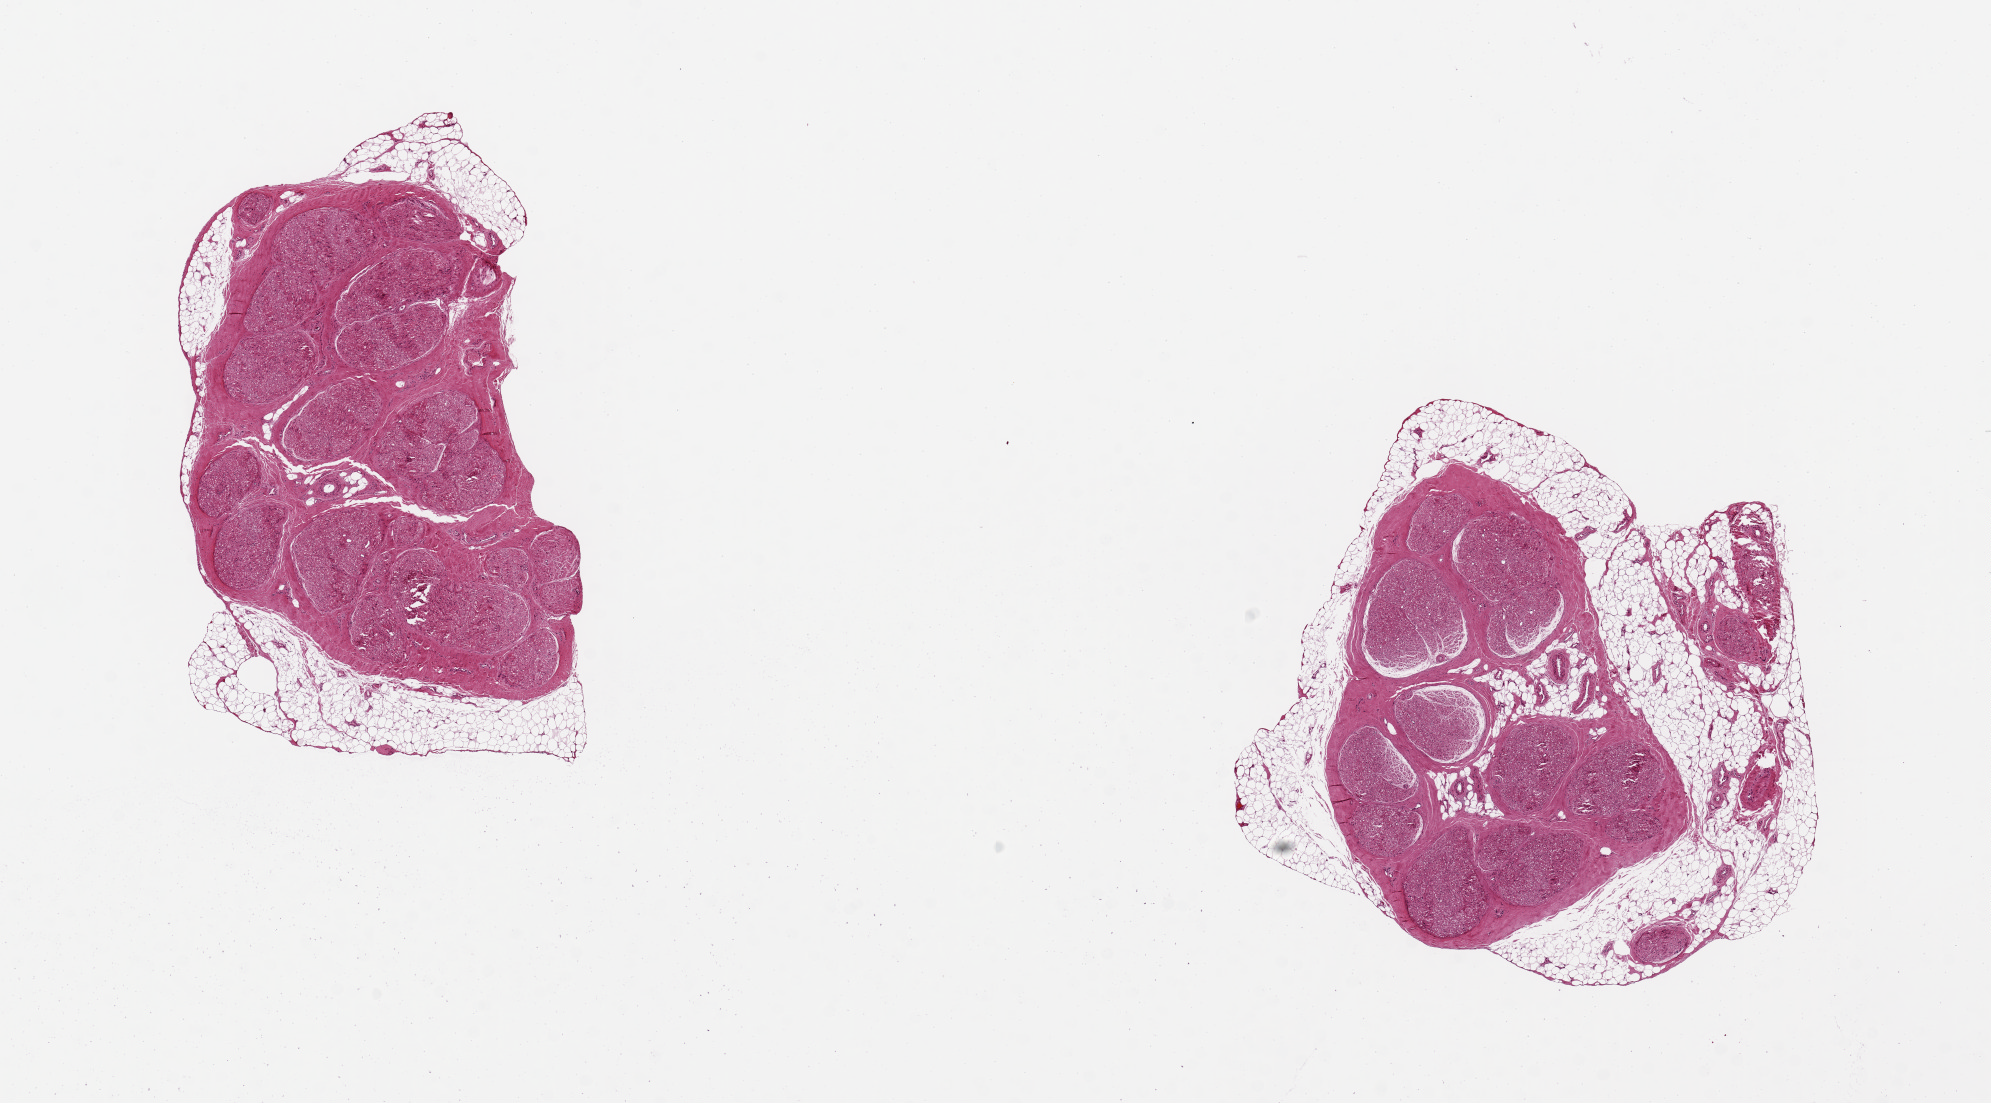
H&E whole-slide image, whole scanned area (about 15.8 x 8.7 mm, from a 20x scan) shown as a low-resolution overview, PAXgene-fixed paraffin-embedded (PFPE) section, target tissue: tibial nerve, donor tissue sample.
Reviewer comment on this tissue sample: 2 pieces 5x3 & 5x4 mm; ~20 & 40% peripheral adipose.